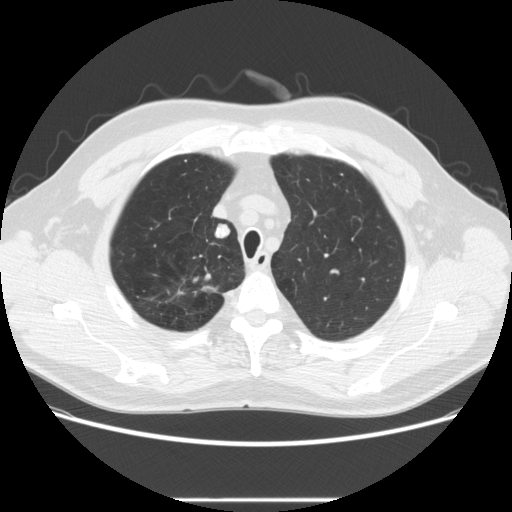
Low-dose screening chest CT, axial slice, baseline annual screen, lung window (W 1500 / L -600 HU), standard (soft-tissue) reconstruction kernel (STANDARD), slice 45 of 270 in the series, 512 × 512 image matrix, field of view 380 × 380 mm. Male participant, aged 64 years at enrolment. Former smoker at enrolment.
2 lesions marked by an expert reader on this slice (largest first), box from (x=168, y=273) to (x=228, y=305) px; (x=203, y=220)–(x=238, y=249). The screening reader recorded 2 non-calcified nodules or masses ≥4 mm on this exam (right upper lobe, right upper lobe); which of them these boxes mark is not recorded. Official screen result: positive, change unspecified: nodule(s) >= 4 mm or enlarging nodule(s), mass(es), or other non-specific abnormalities suspicious for lung cancer. Lung cancer was diagnosed 753 days after this screen: adenocarcinoma, NOS, right upper lobe, moderately differentiated (G2), stage IA (AJCC 6th edition), 14 mm at pathology.